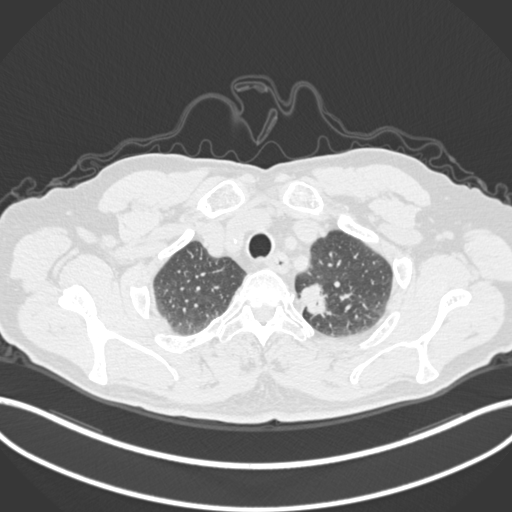
Chest CT, one axial slice. Position 279 of 306 along the scan axis. Reconstruction kernel B30f. 120 kVp. Lung window (W 1500 / L -600 HU). 1 mm slice thickness. 512 × 512 image matrix. Male patient, age 64 years. Case-level facts recorded for this patient, not image findings: clinical TNM (as recorded): T1c N0 M0.
Outlined on this slice (rectangle marked by the reading radiologist):
- lung tumour (recorded histology: adenocarcinoma): bounding box [x1, y1, x2, y2] px = [300, 282, 336, 321]